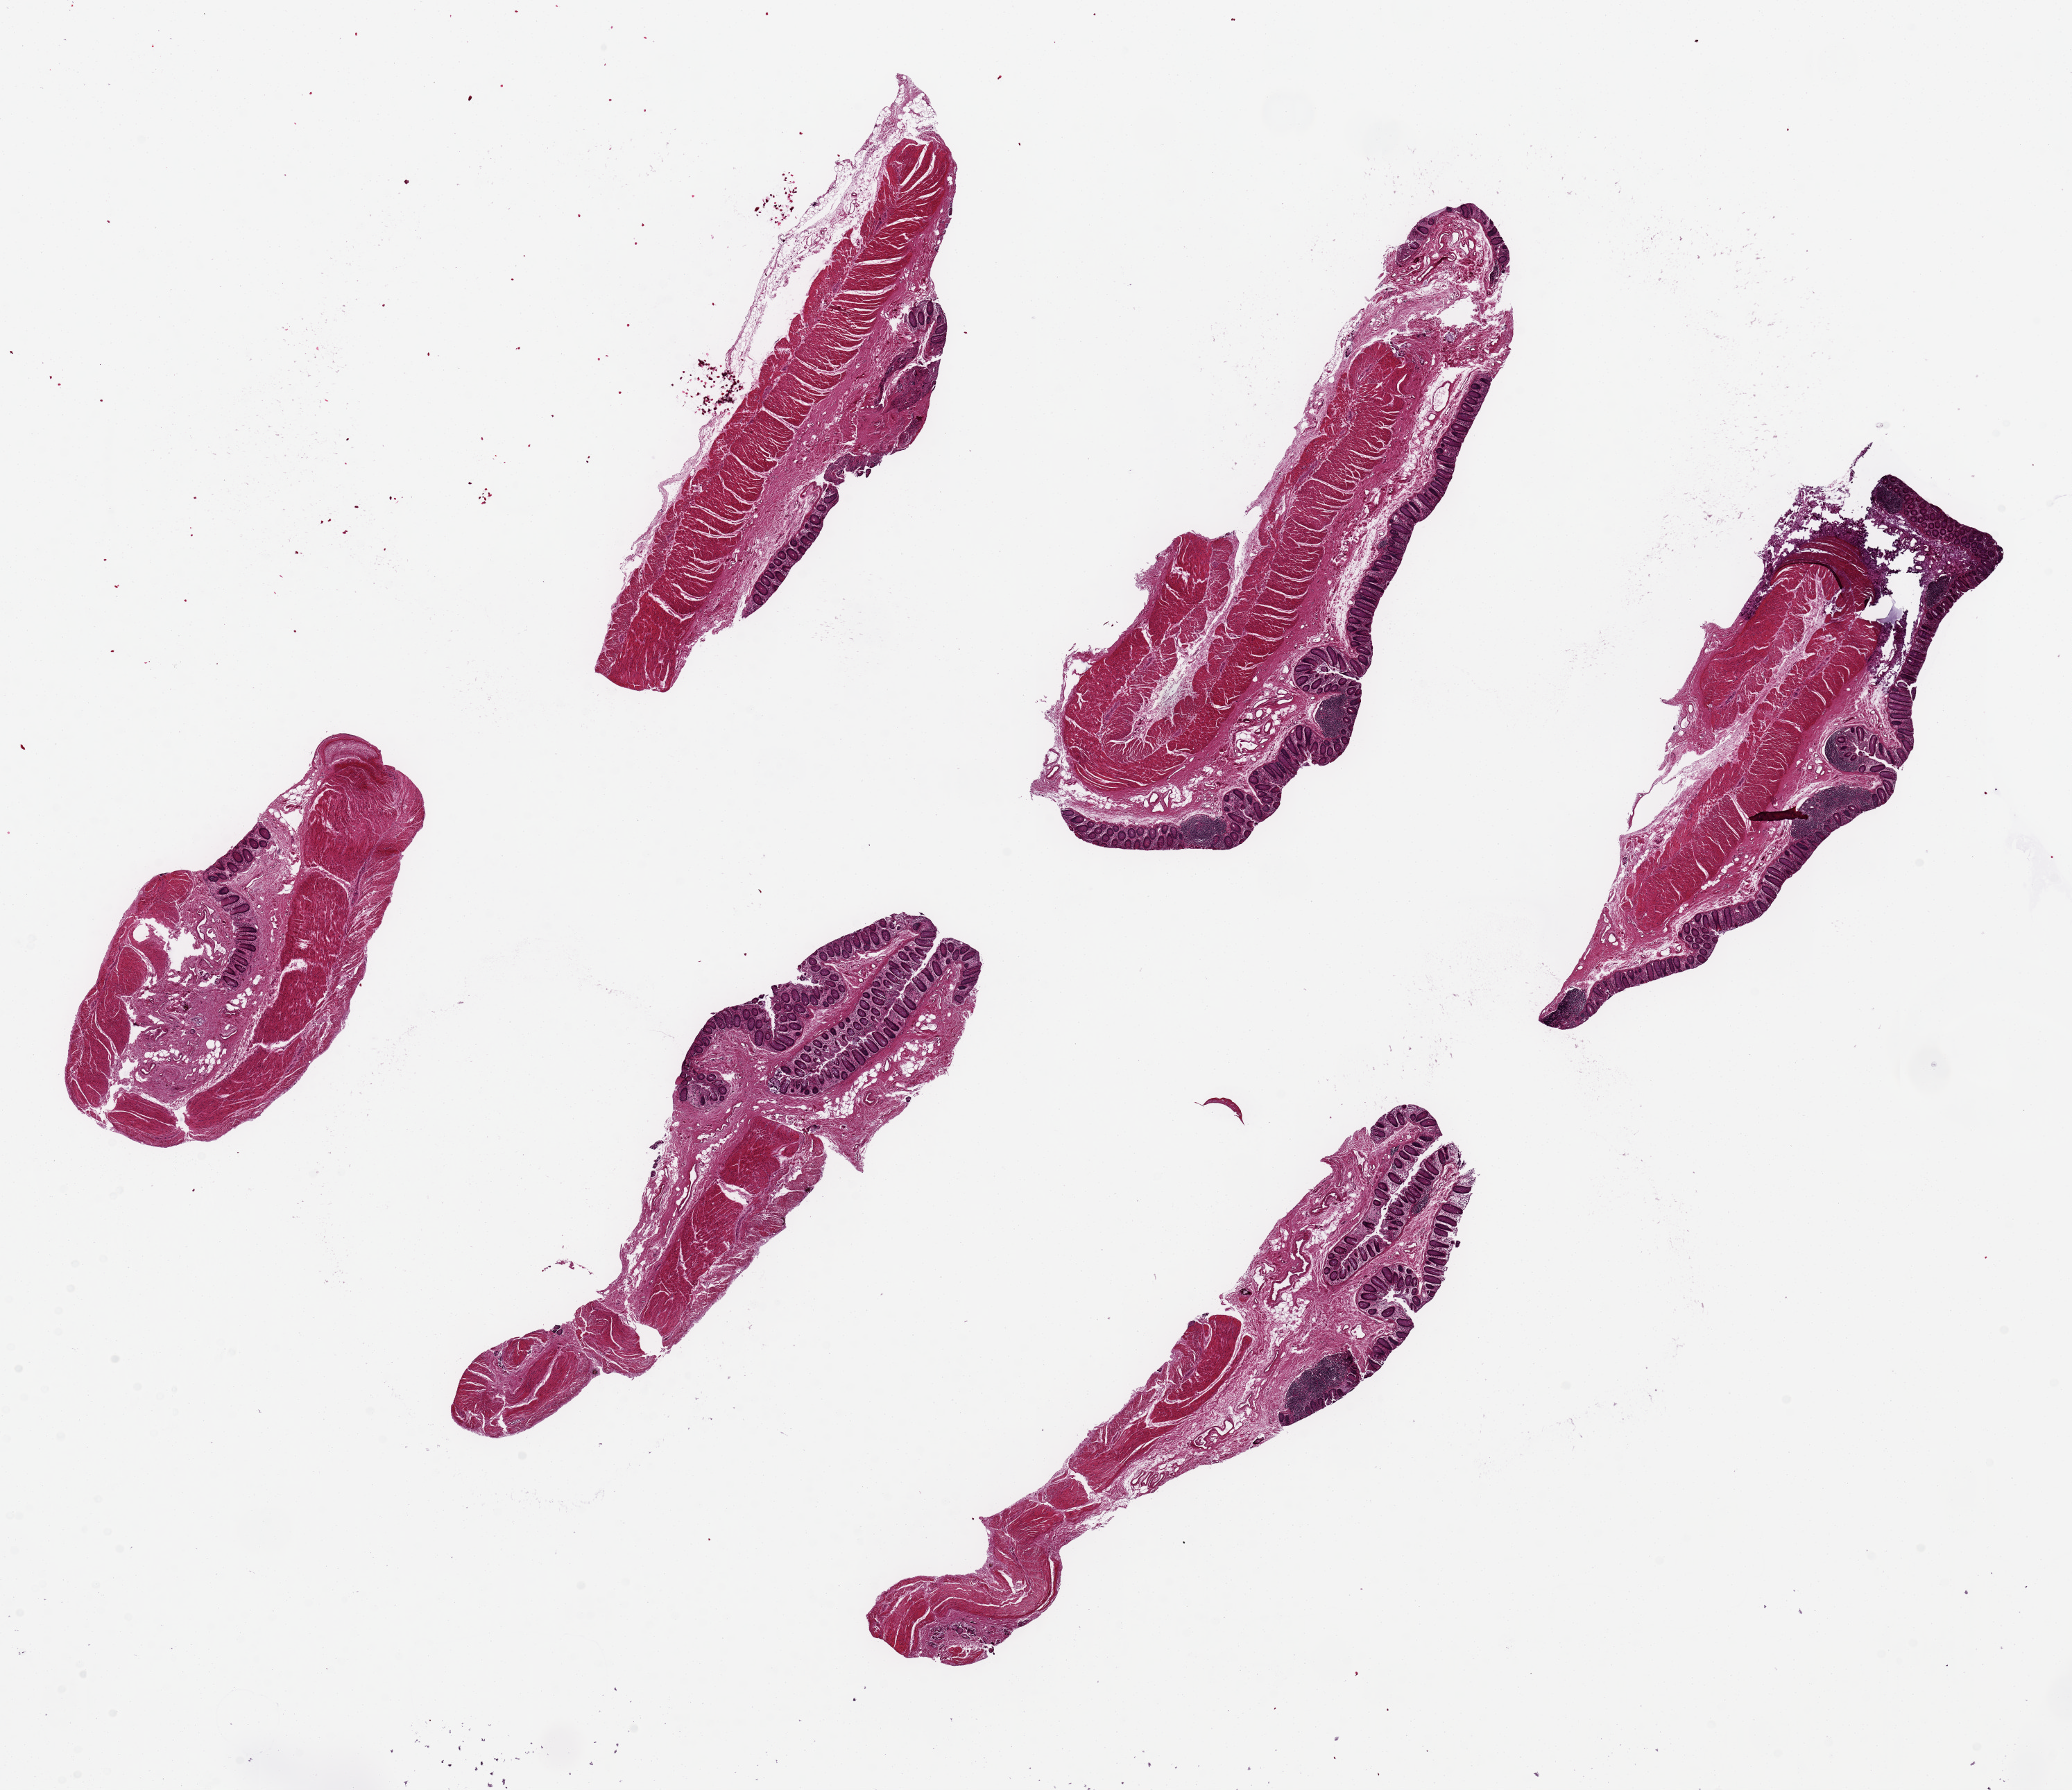
Digitized hematoxylin and eosin (H&E)-stained section, a low-resolution overview of the entire scanned area, about 23.6 x 20.4 mm (from a 20x scan), PAXgene-fixed paraffin-embedded (PFPE) section, section of transverse colon (target tissue), tissue donor sample.
Reviewer comment on this tissue sample: 6 pieces, ~8x2mm. Mucosa moderately well preserved, ~10-15% of thickness.